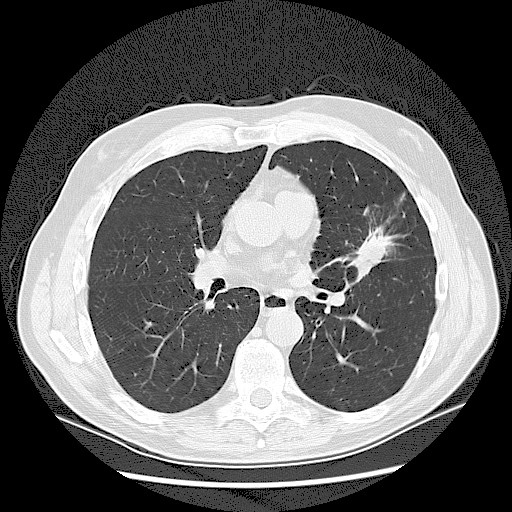
Axial slice from a low-dose chest CT screening exam. Baseline annual screen. Lung window (W 1500 / L -600 HU). Male participant, aged 65 years at enrolment.
- Expert reader's lesion annotation, box from (x=346, y=219) to (x=399, y=266) px.
- Screening reader's record for this exam (one nodule recorded; not confirmed to be the boxed lesion): non-calcified nodule or mass ≥4 mm, left upper lobe, 37 × 27 mm, spiculated (stellate) margins, soft tissue attenuation.
- Official screen result: positive, change unspecified: nodule(s) >= 4 mm or enlarging nodule(s), mass(es), or other non-specific abnormalities suspicious for lung cancer.
- Later outcome: lung cancer diagnosed 56 days after this screen — non-small cell carcinoma, poorly differentiated (G3), stage IA (AJCC 6th edition).